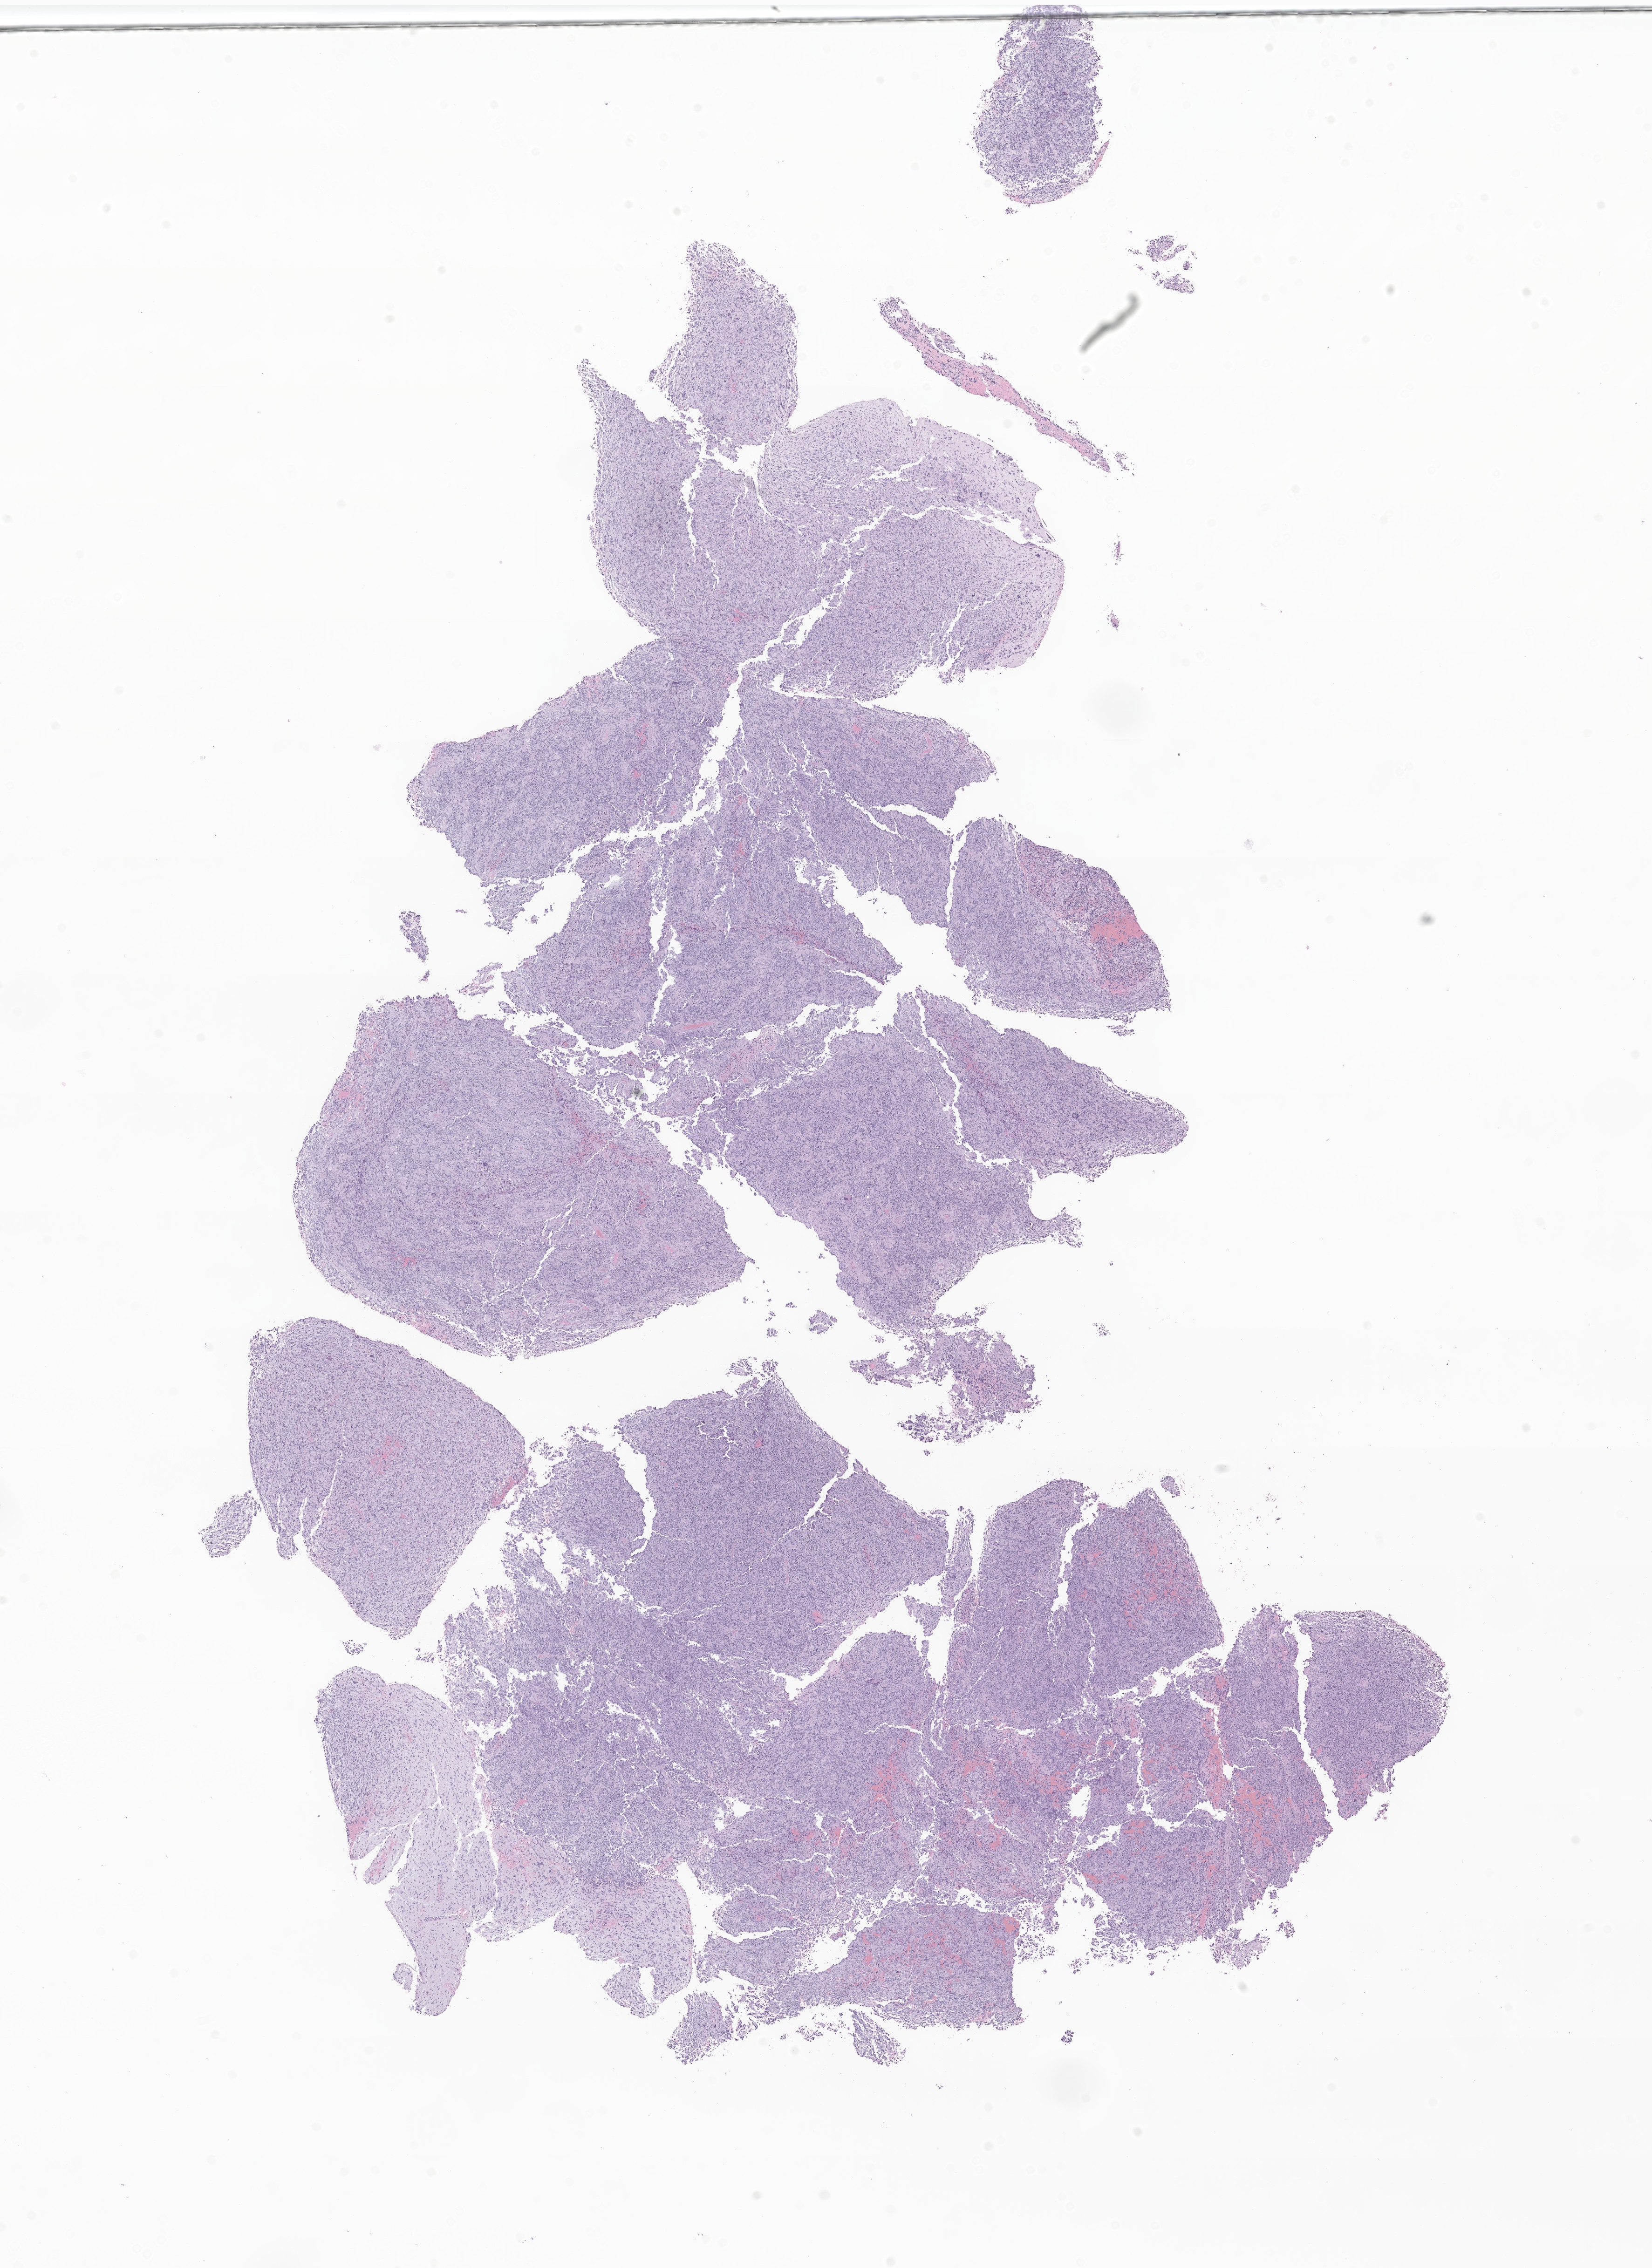
Whole-slide image, haematoxylin and eosin stain of tumor tissue from the frontal lobe, low-resolution overview of the scanned area, about 14.9 x 20.5 mm. Formalin-fixed, paraffin-embedded (FFPE) tissue. Patient female; age 199 months (16 years 7 months).
Diagnosis: Glioma, malignant.